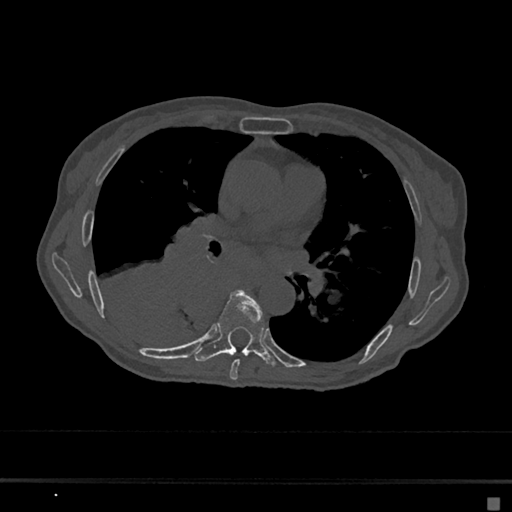
CT including the spine, one axial slice. Slice 387 of 797 in the series (ordered by position). Reconstruction kernel Br40s/3. 120 kVp. Bone window (W 1800 / L 400 HU). 0.5 mm slice thickness. 512 × 512 image matrix. Female patient, age 68 years. Case-level facts recorded for this patient, not image findings: primary cancer: renal.
Annotated regions visible in this slice (semi-automatic segmentation, software-assisted and operator-edited):
- T6 vertebra: bounding box (x1, y1, x2, y2) in pixels: (229, 359, 240, 380)
- T7 vertebra: (194, 291, 276, 366)